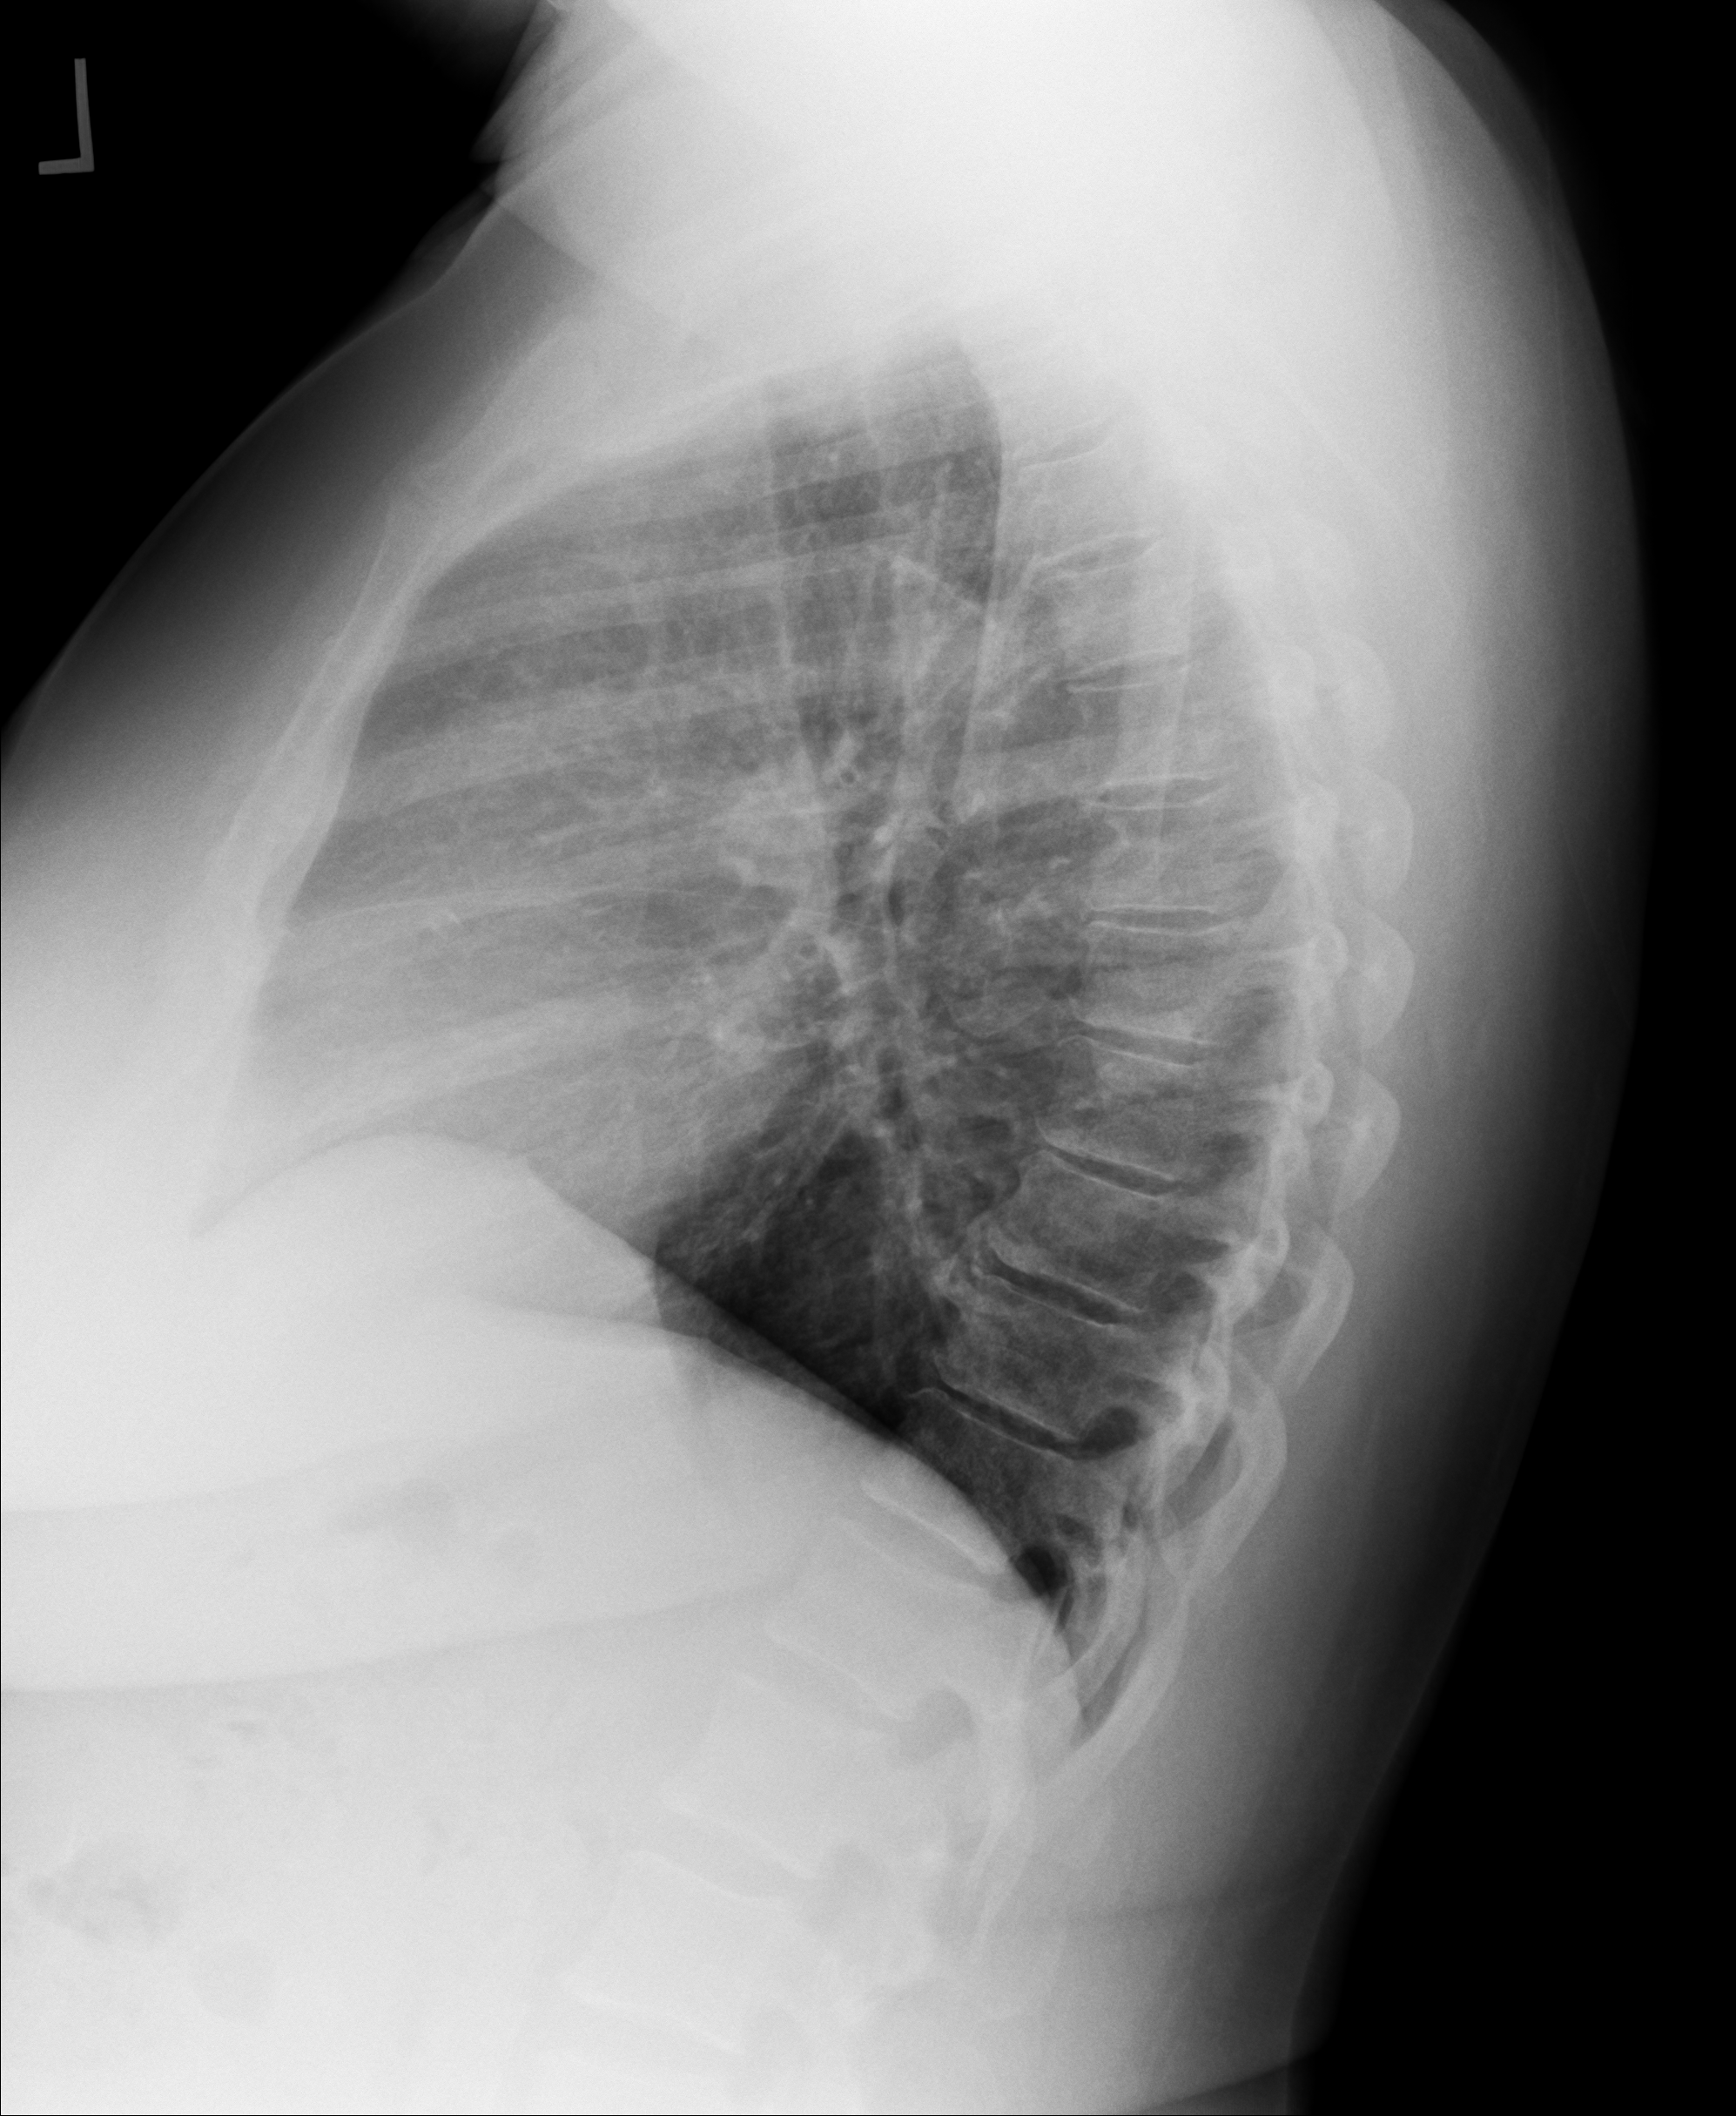
Chest X-ray. Female patient, age 61 years; imaged 51 days after the COVID-19 diagnosis.
Radiologist's key findings for this exam: clearing of previous ill-defined opacities at lung base.